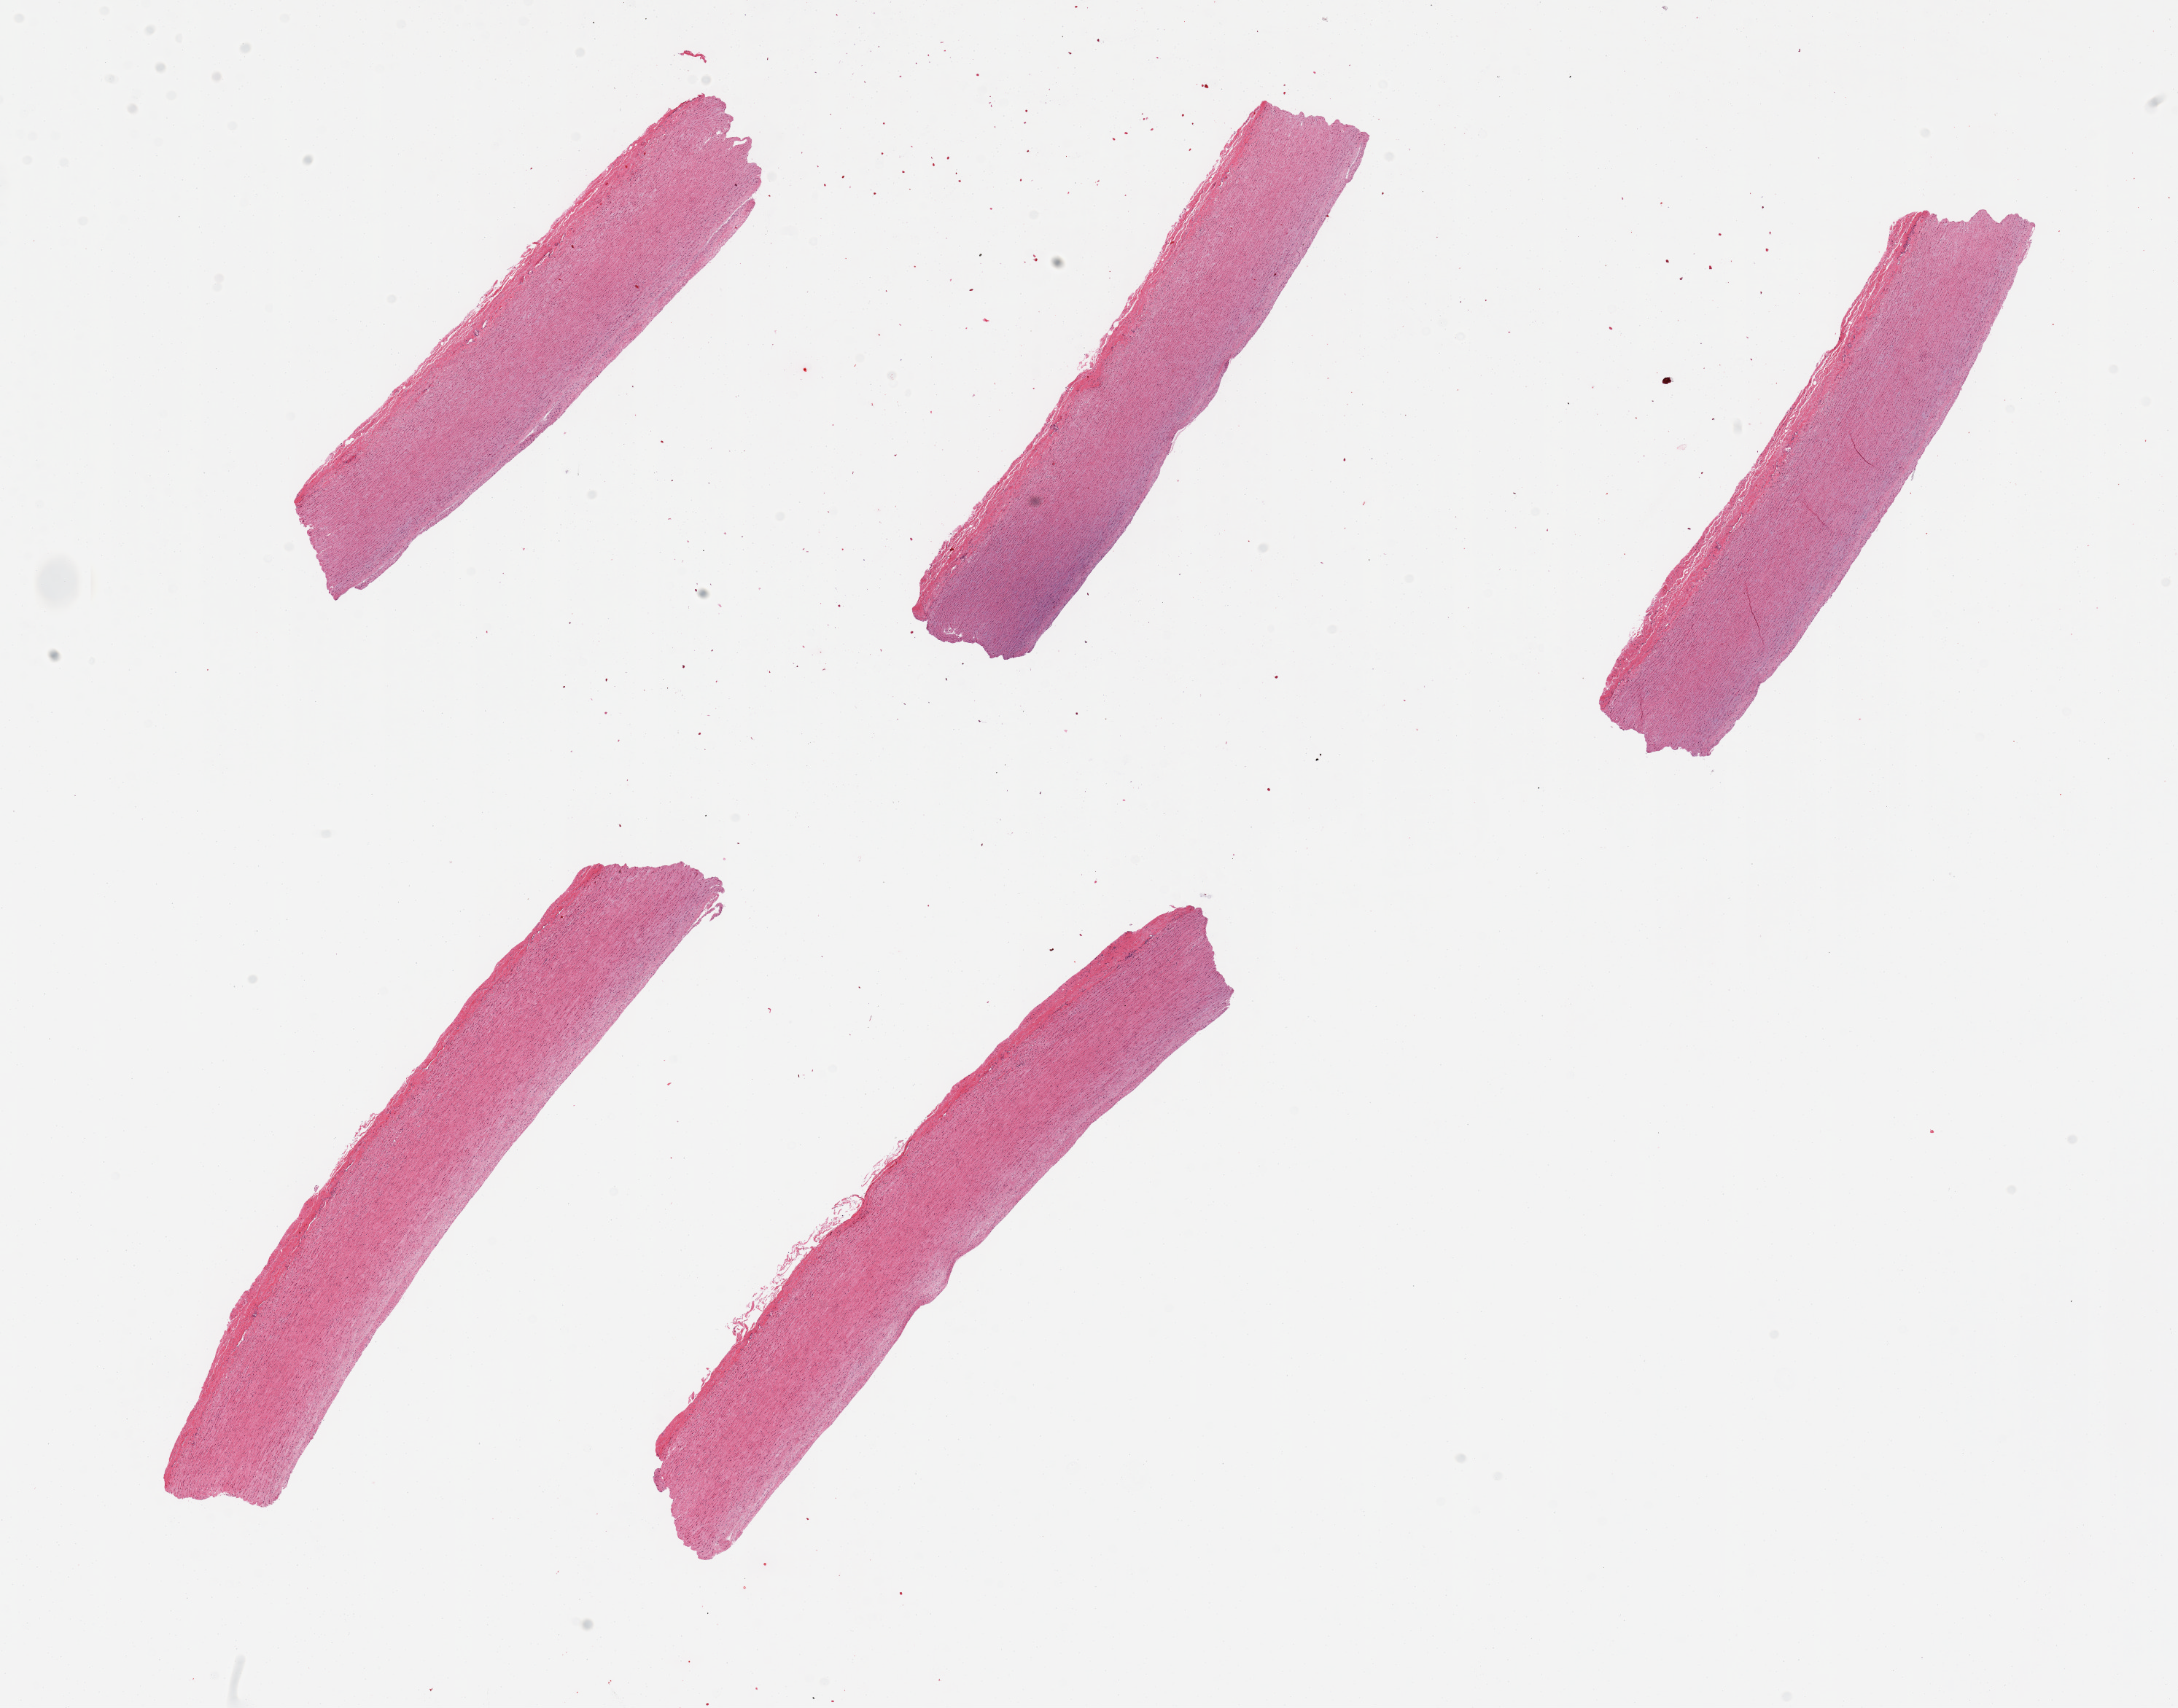
Hematoxylin and eosin (H&E) whole-slide image, whole scanned area (about 23.6 x 18.5 mm, slide scanned at 20x) shown as a low-resolution overview, PAXgene-fixed paraffin-embedded (PFPE) section, section of aorta (target tissue), tissue donor sample. Donor: male.
* review note (as recorded): 5 pieces; well trimmed, no plaques